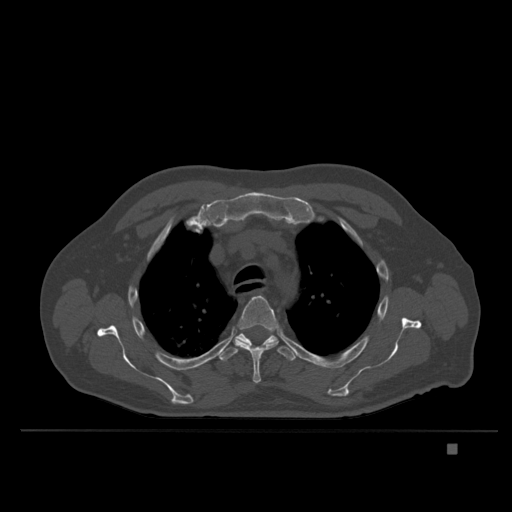
CT including the spine, one axial slice. Position 283 of 435 along the scan axis. Bone window (W 1800 / L 400 HU). 1.5 mm slice thickness. 512 × 512 image matrix, field of view 434 × 434 mm. Male patient, age 73 years. Case-level facts recorded for this patient, not image findings: primary cancer: skin.
Annotated regions visible in this slice (semi-automatically segmented with operator editing):
- T4 vertebra: bounding box <233,296,278,384> (left, top, right, bottom; pixels)
- T5 vertebra: <220,331,295,363>